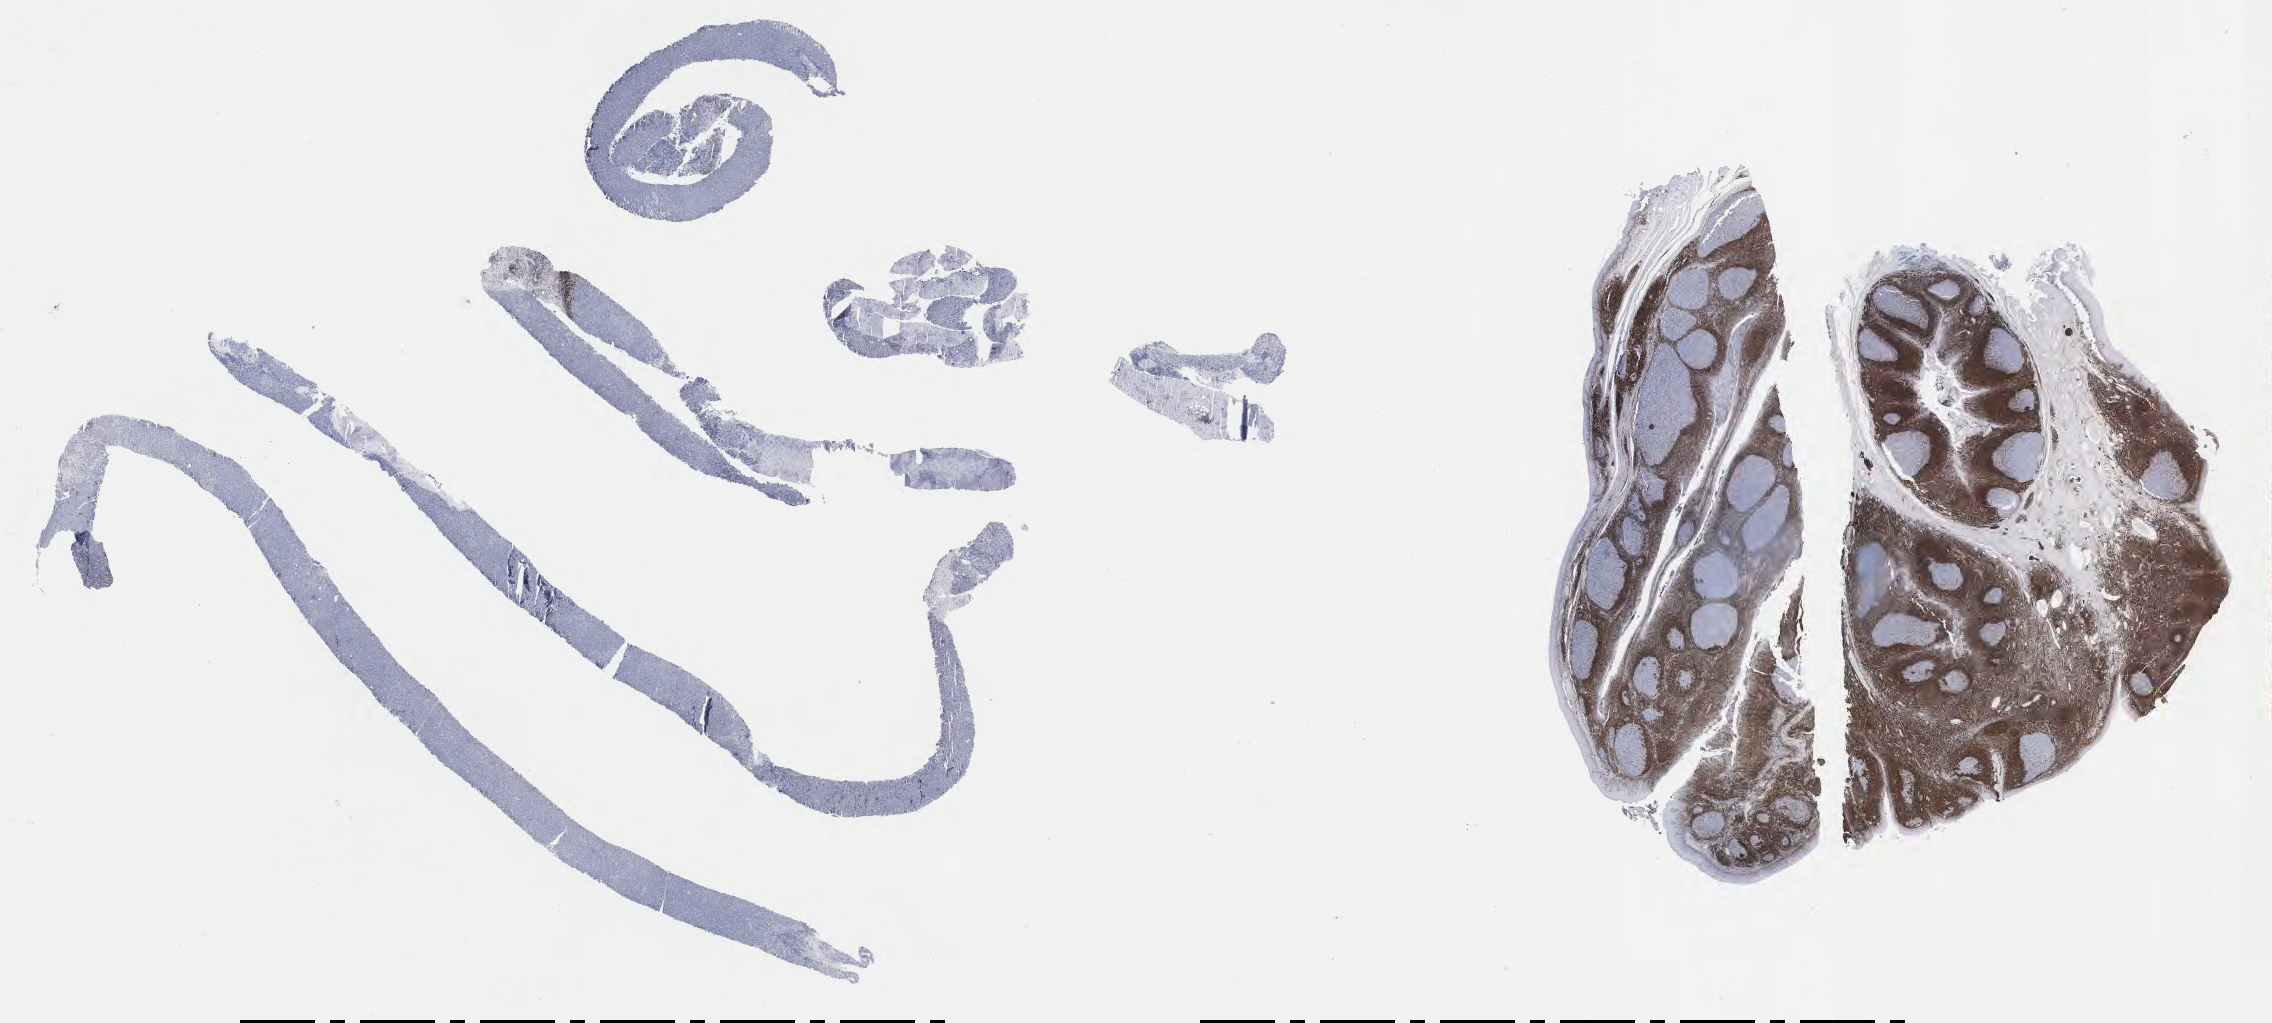
IHC for BCL2, whole-slide image, a low-resolution overview of the entire scanned area, about 36.7 x 16.5 mm; specimen: tumor tissue. Patient male; age 45 years.
Histologic diagnosis: Burkitt lymphoma, NOS.